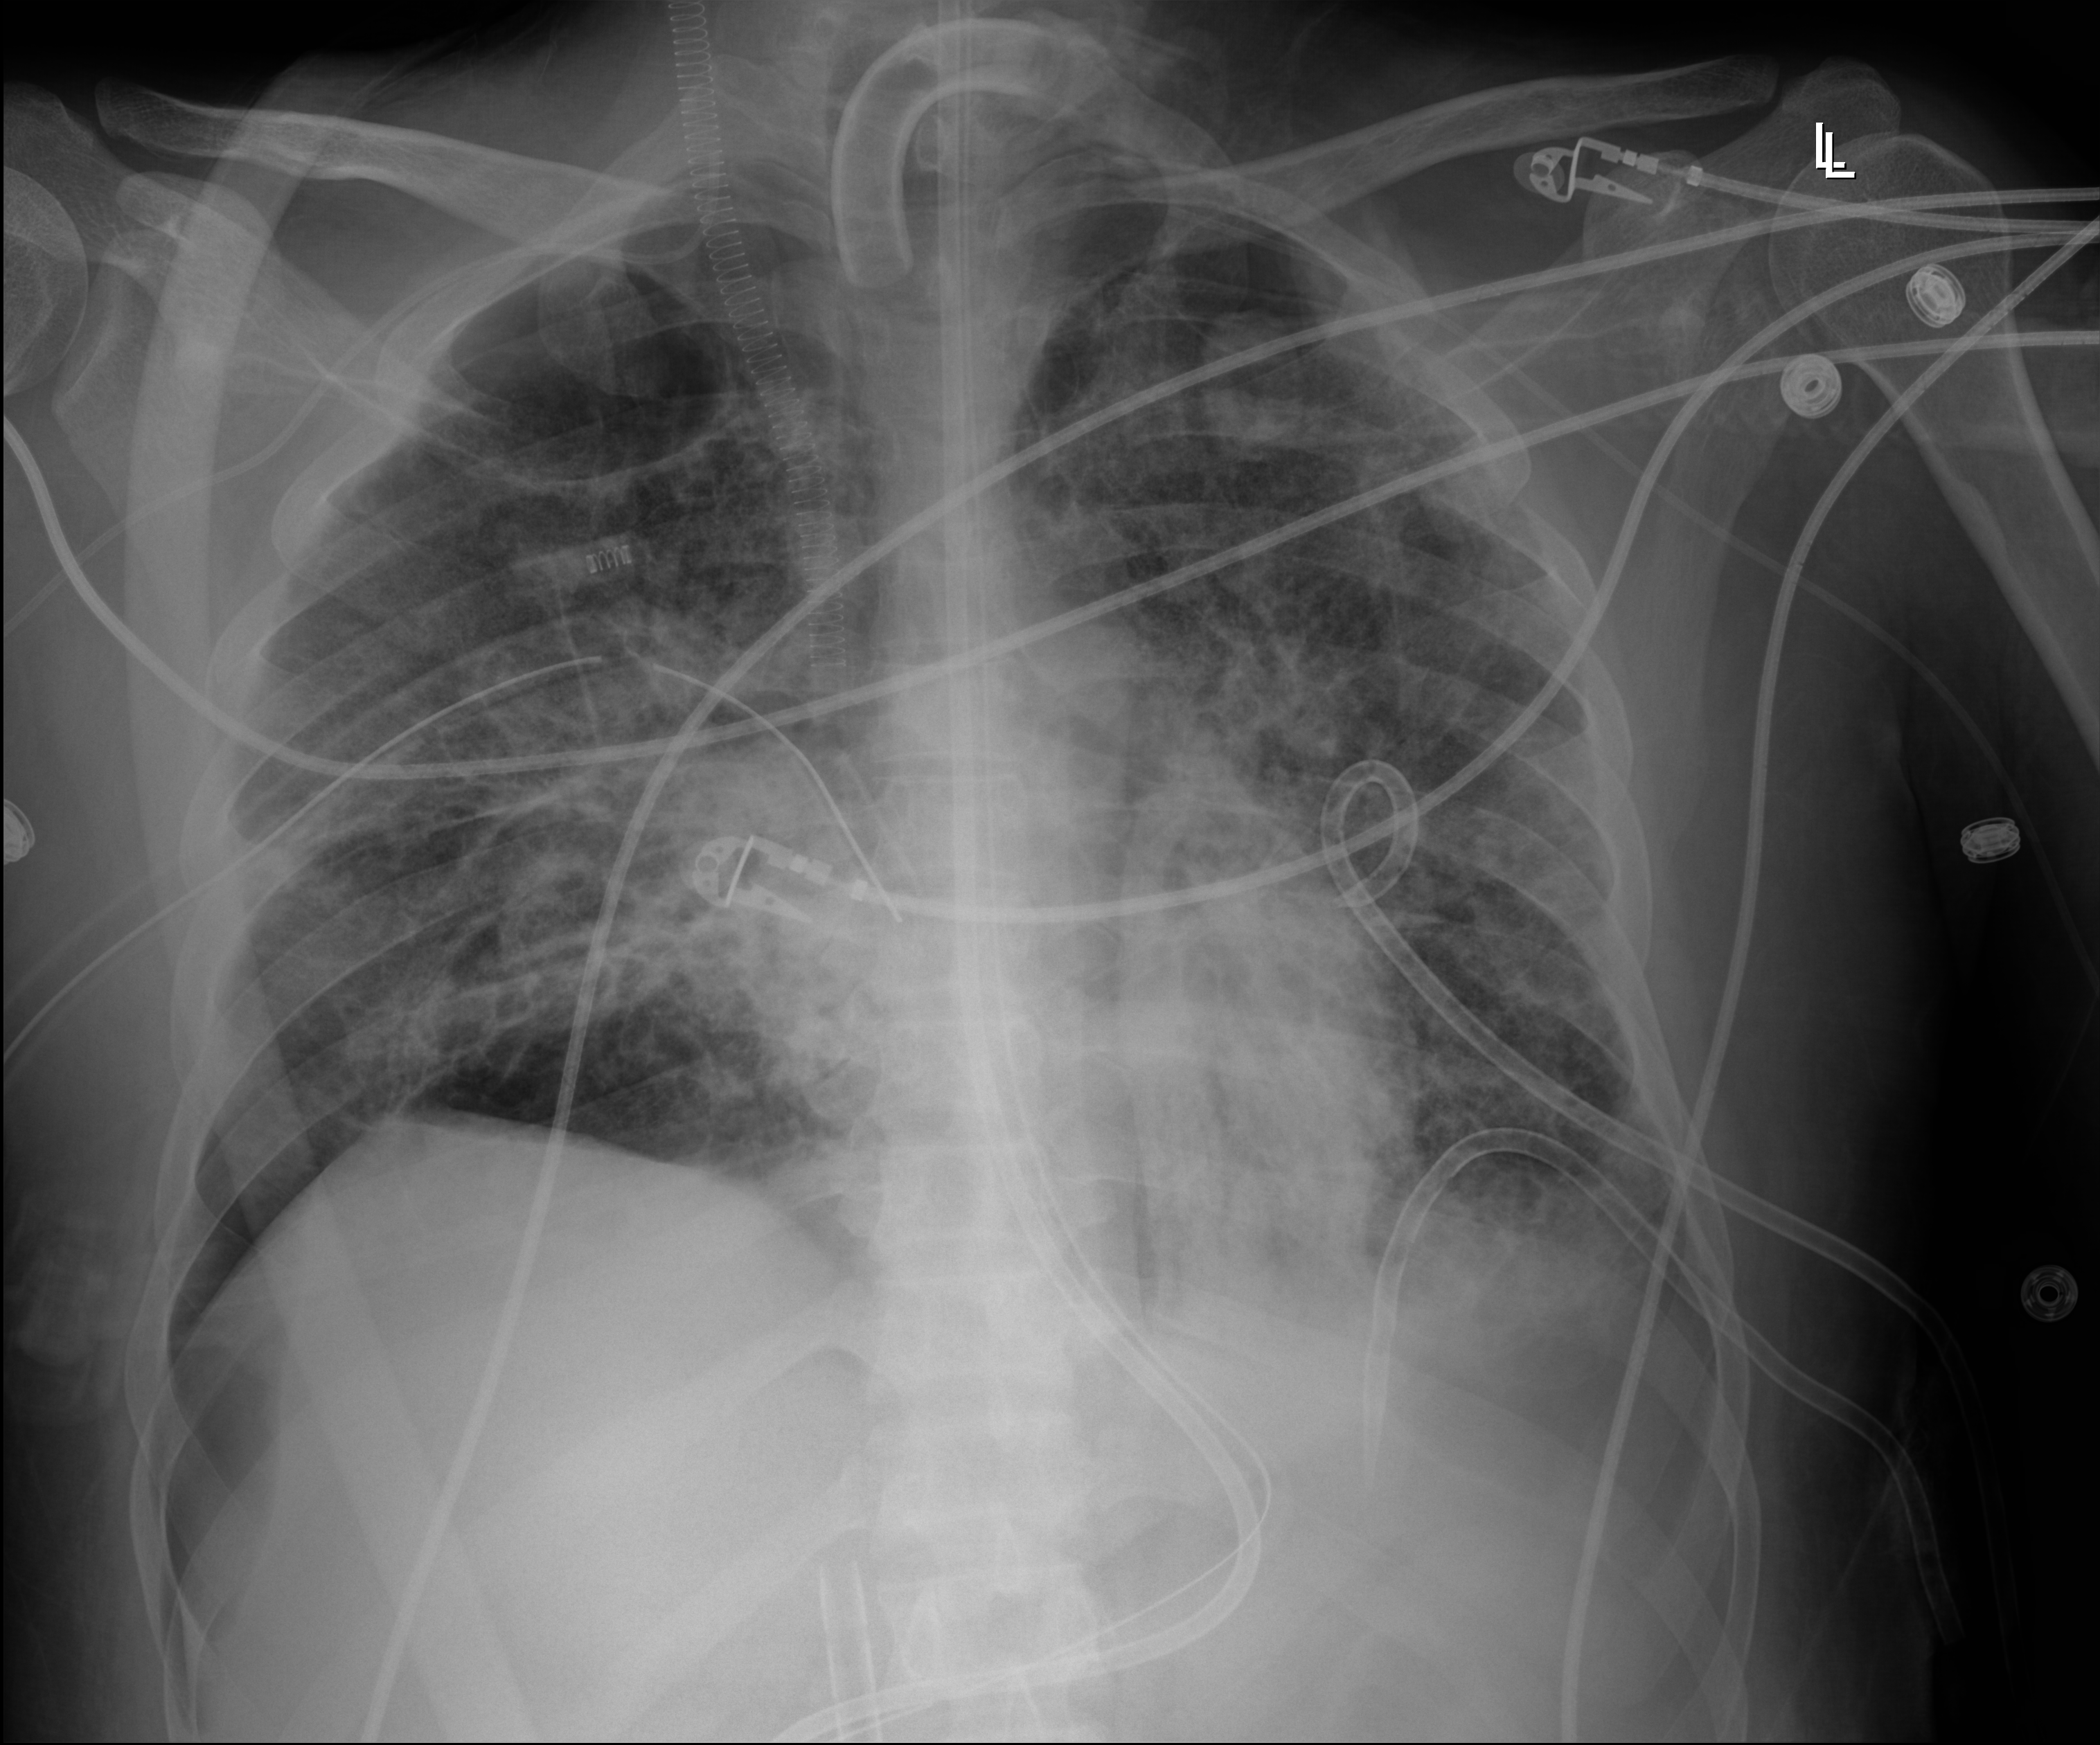
Bedside chest radiograph (digital radiography); anteroposterior (AP) projection. Patient hospitalised with COVID-19, aged 18–59 years.
Hospital-stay facts (about this admission, not read from this image; timing relative to this image not recorded):
- chronic kidney disease (admission record): no
- admitted to intensive care during this hospital stay: yes